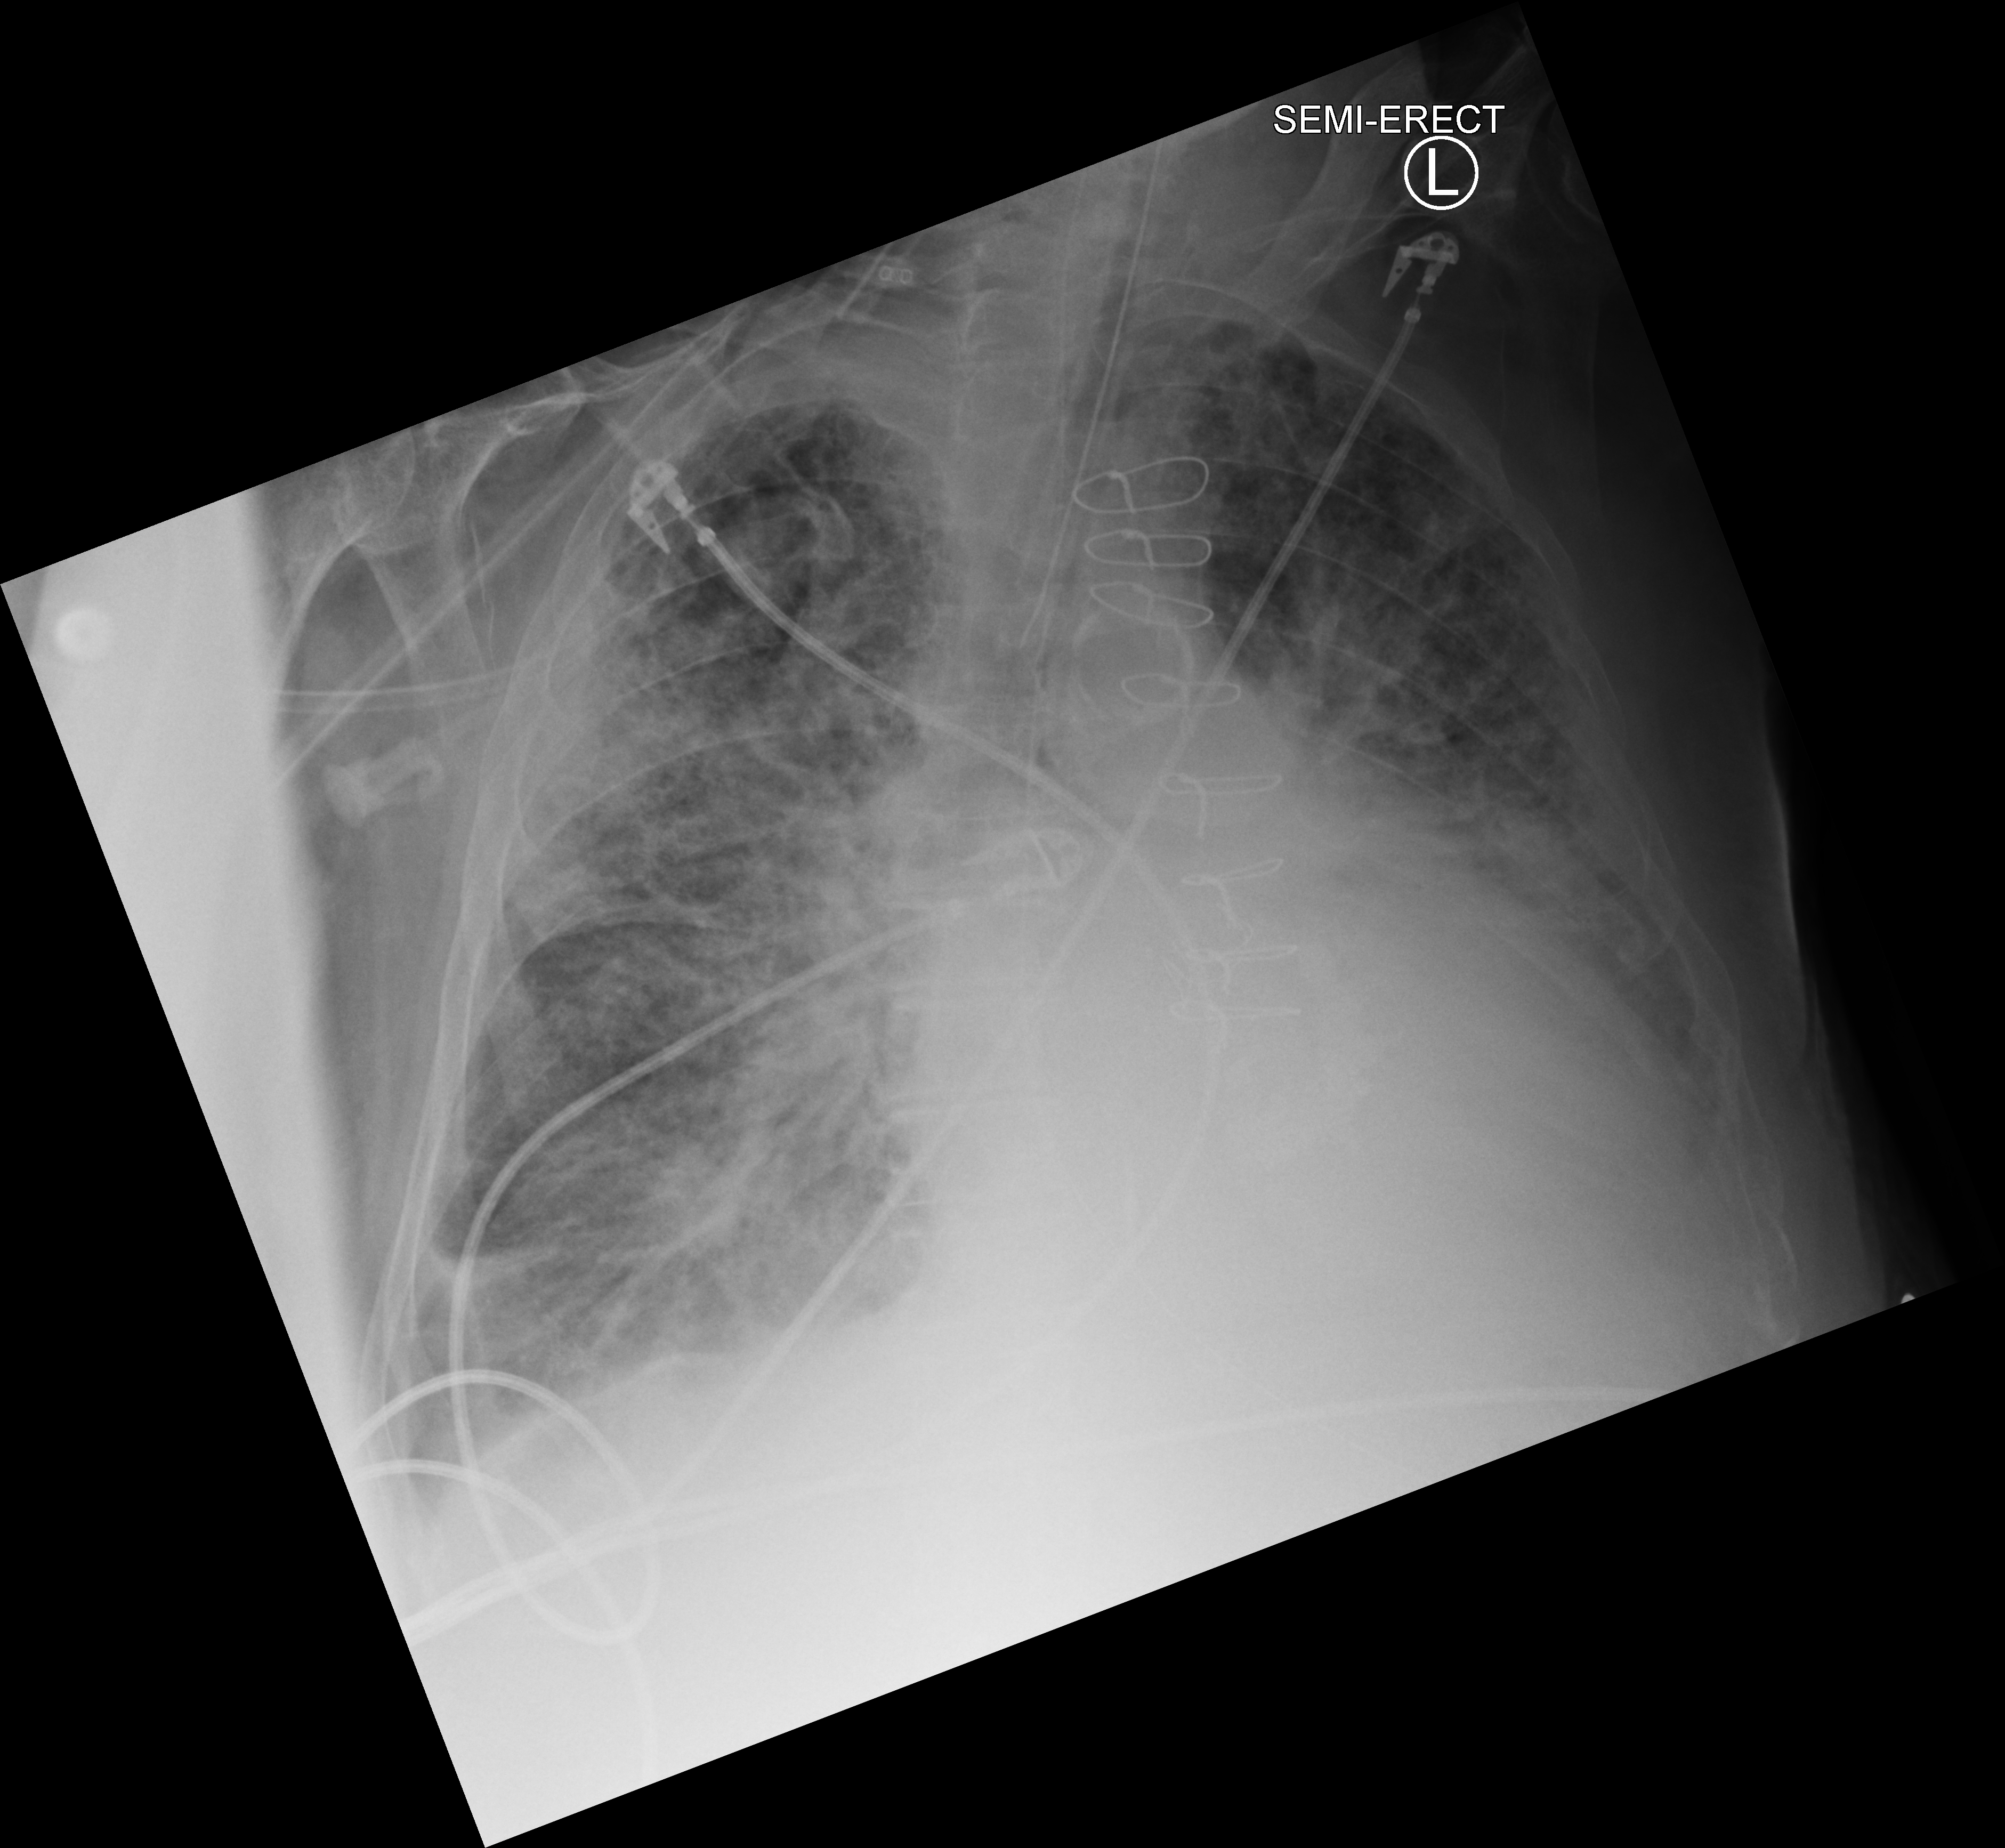
Bedside chest radiograph (computed radiography); anteroposterior (AP) projection. Male patient hospitalised with COVID-19, age 75–90 years.
From the hospital-stay record, not from the radiograph (when in the stay this image was taken is not recorded): mechanically ventilated during this hospital stay: yes; length of hospital stay: 40 days; admitted to intensive care during this hospital stay: yes.